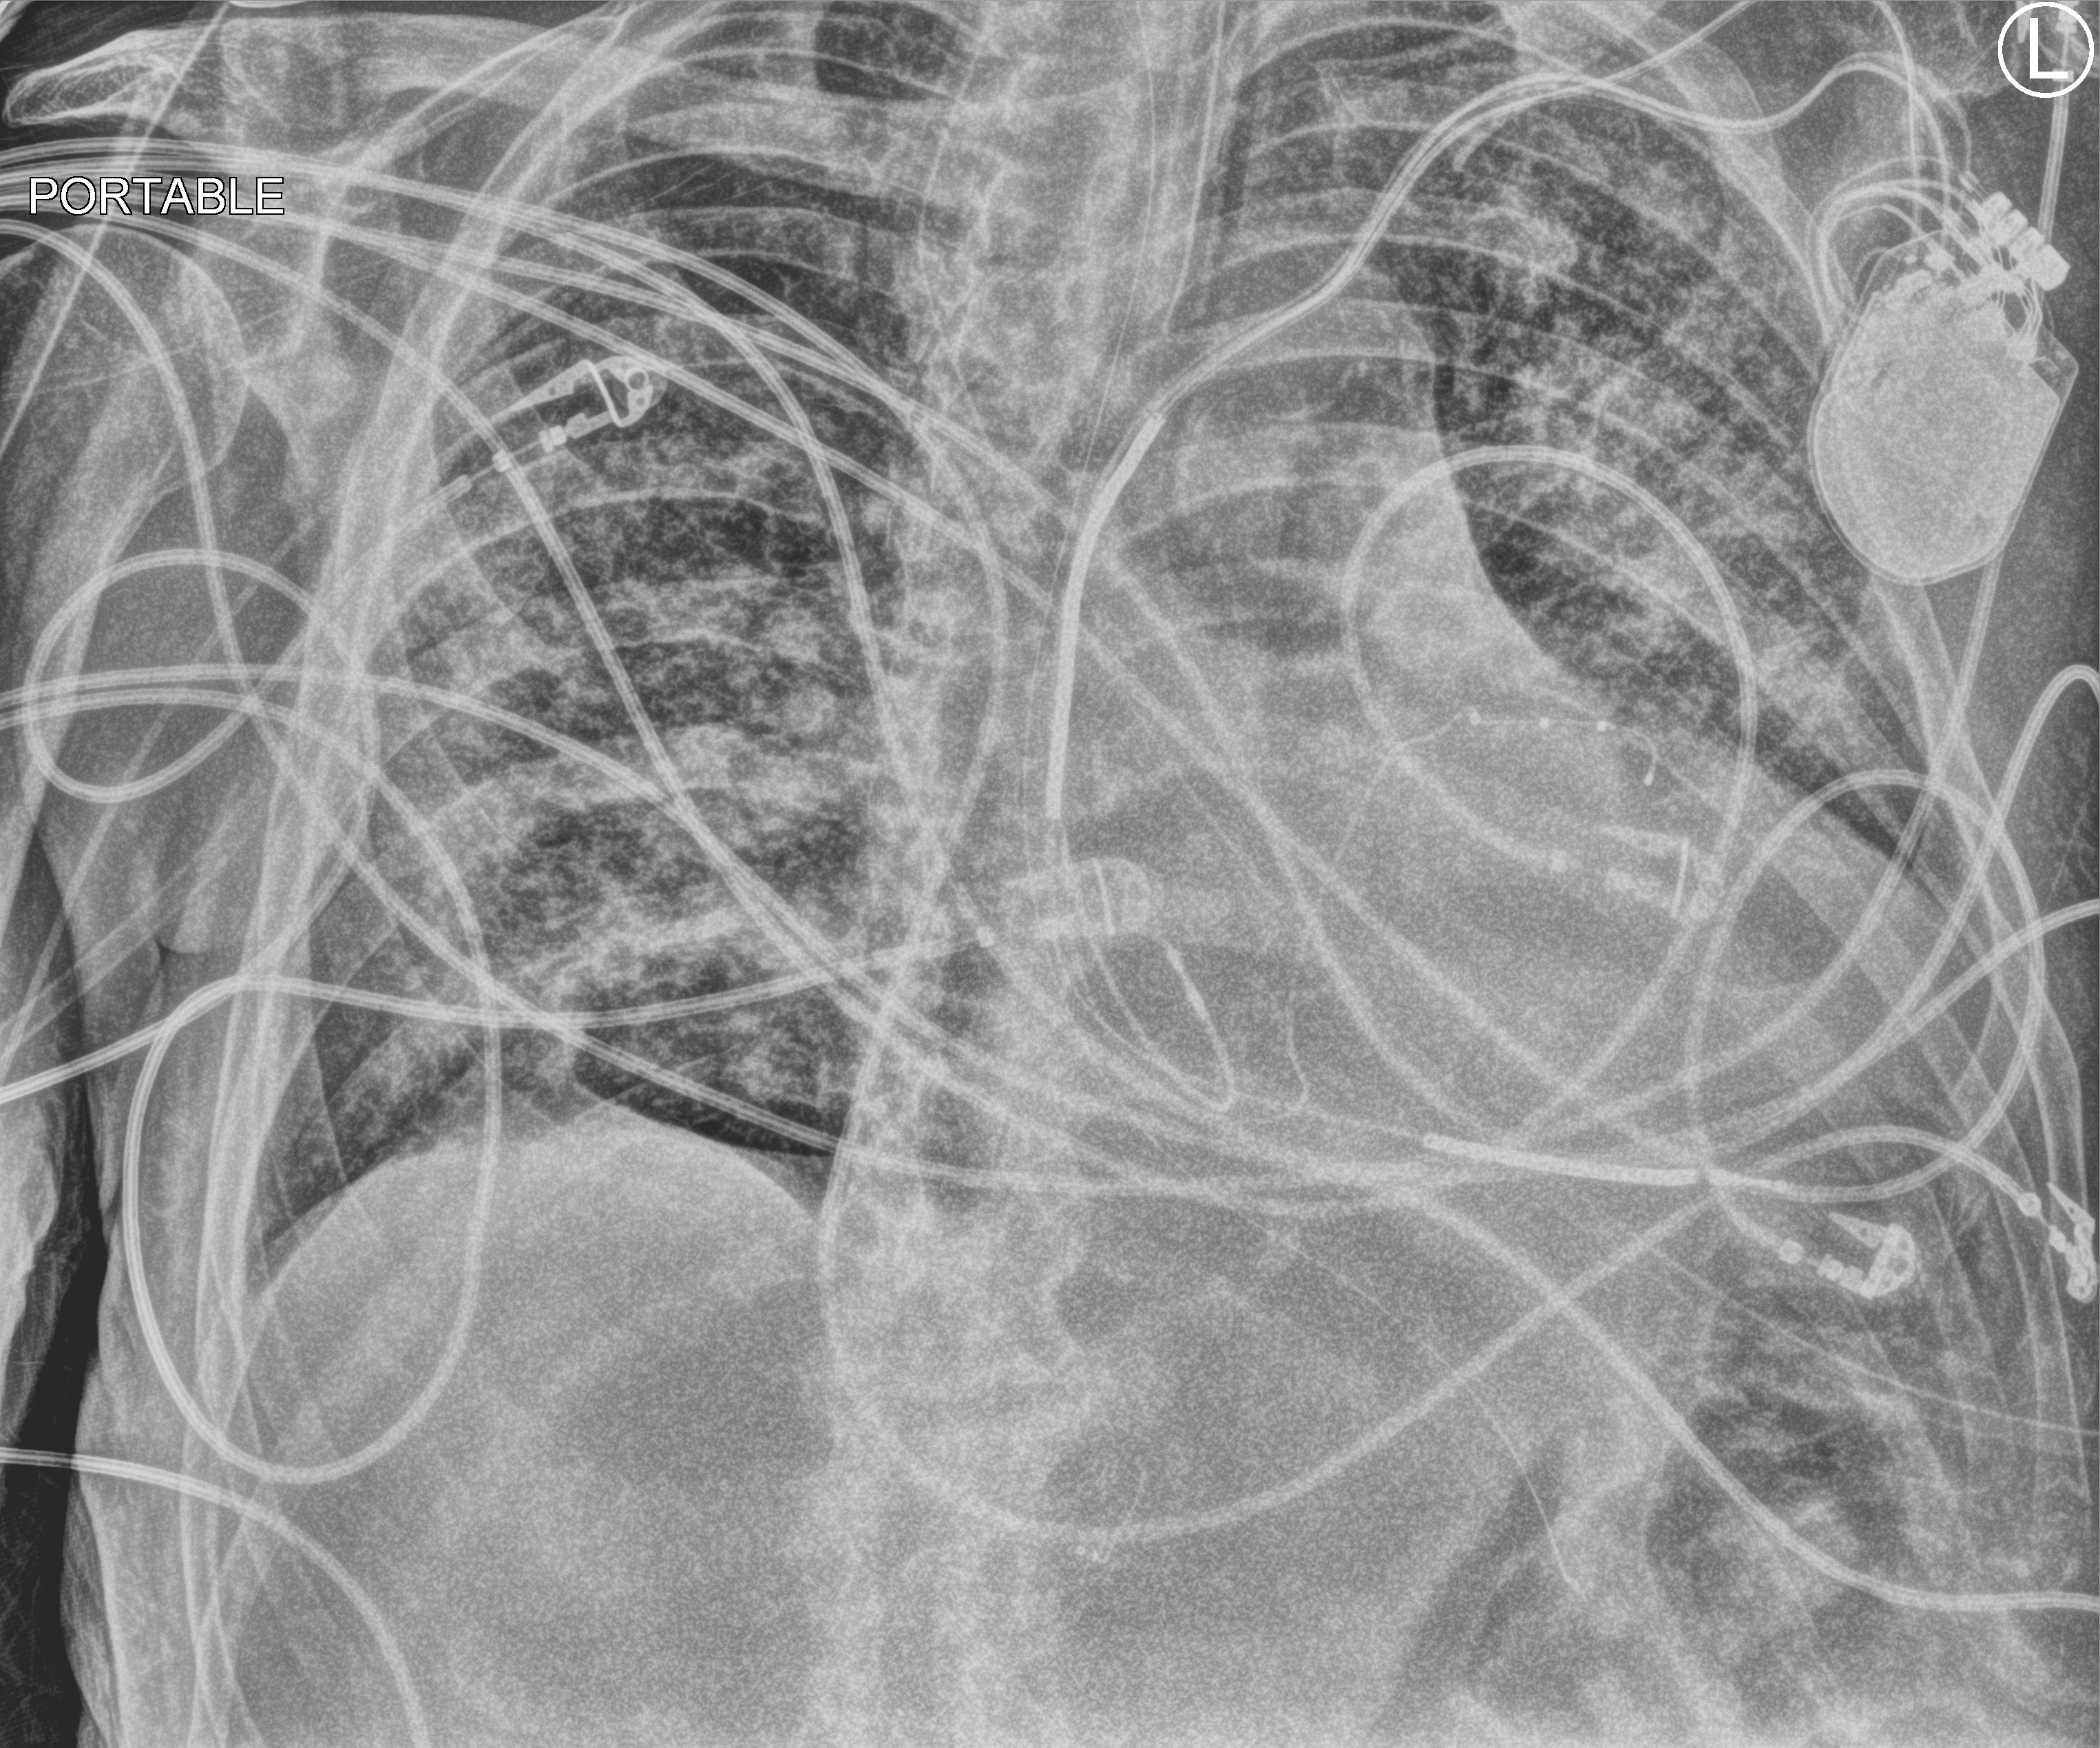
Bedside chest radiograph (computed radiography); anteroposterior (AP) projection. Patient hospitalised with COVID-19; male, aged 60–74 years.
Hospital-stay facts (about this admission, not read from this image; timing relative to this image not recorded): admitted to intensive care during this hospital stay: yes.